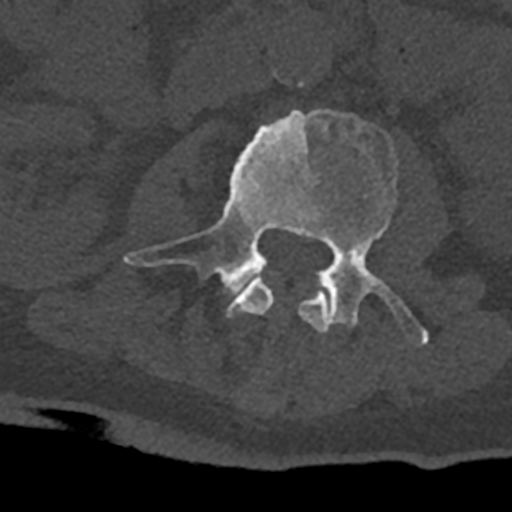
CT including the spine, one axial slice; slice 334 of 797 in the series (ordered by position); reconstruction kernel Br40s/3; 120 kVp; bone window (W 1800 / L 400 HU); 0.5 mm slice thickness; 512 × 512 image matrix, field of view 160 × 160 mm. Male patient, age 74 years. From the clinical record (not read from this slice): primary cancer: renal.
Annotated regions visible in this slice (semi-automatic segmentation, software-assisted and operator-edited):
- L2 vertebra: bounding box <226,278,330,333> (left, top, right, bottom; pixels)
- L3 vertebra: <123,109,429,345>